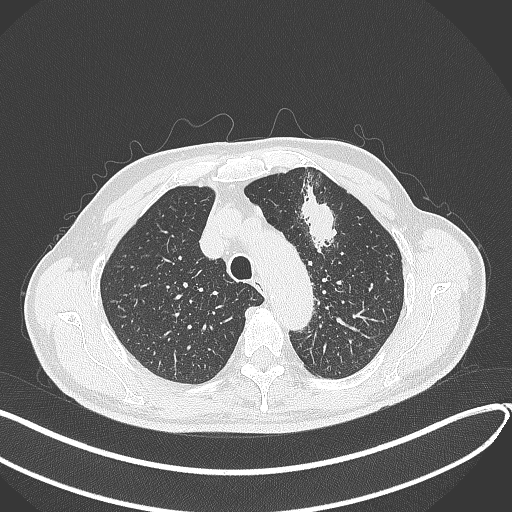
Chest CT, one axial slice; slice 325 of 459 in the series (ordered by position); reconstruction kernel B70f; lung window (W 1500 / L -600 HU); 1 mm slice thickness; 512 × 512 image matrix. Patient: male, 74 years. Case-level facts recorded for this patient, not image findings: clinical TNM (as recorded): T2b N0 M1c.
Outlined on this slice (rectangle marked by the reading radiologist):
- lung tumour (recorded histology: adenocarcinoma): bounding box <297,181,347,257> (left, top, right, bottom; pixels)